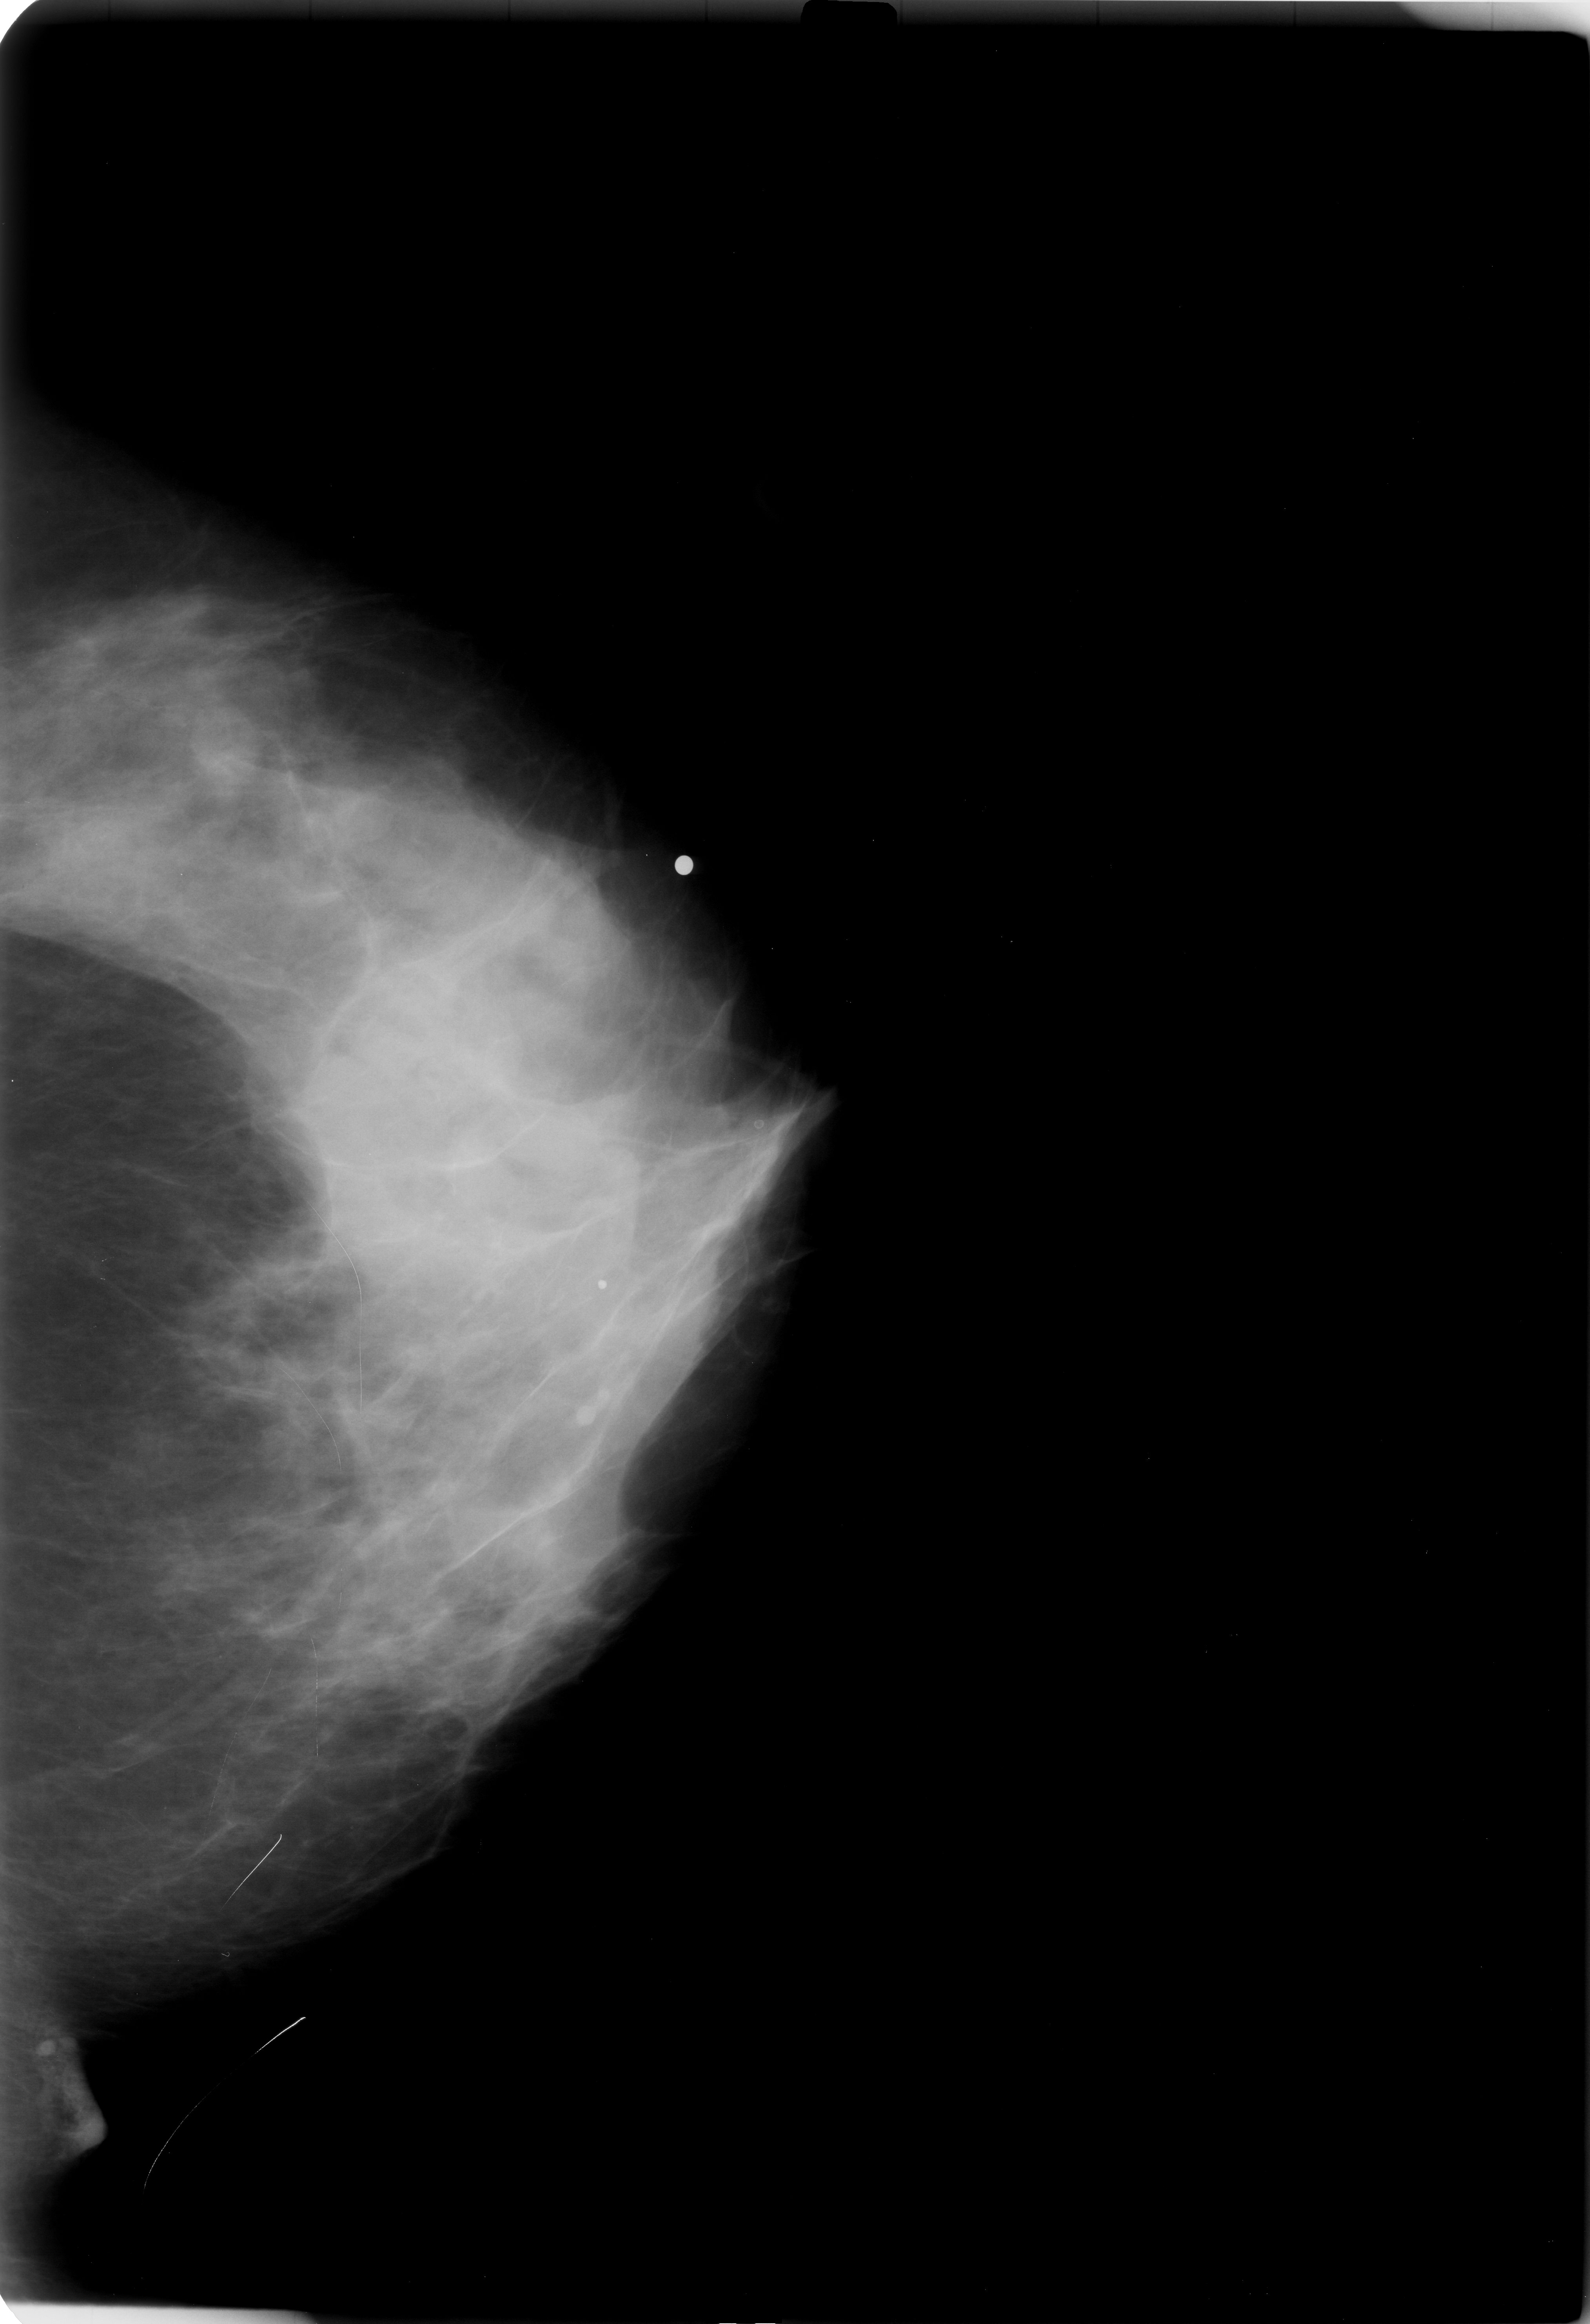
Digitized screen-film mammogram; left breast; craniocaudal (CC) view; BI-RADS breast density category 4 (scale 1–4).
- Finding: mass, shape focal asymmetric density; BI-RADS assessment category 3; subtlety rating 1 on a 1 (subtle) to 5 (obvious) scale; pathology result (as recorded, not read from the image): malignant.